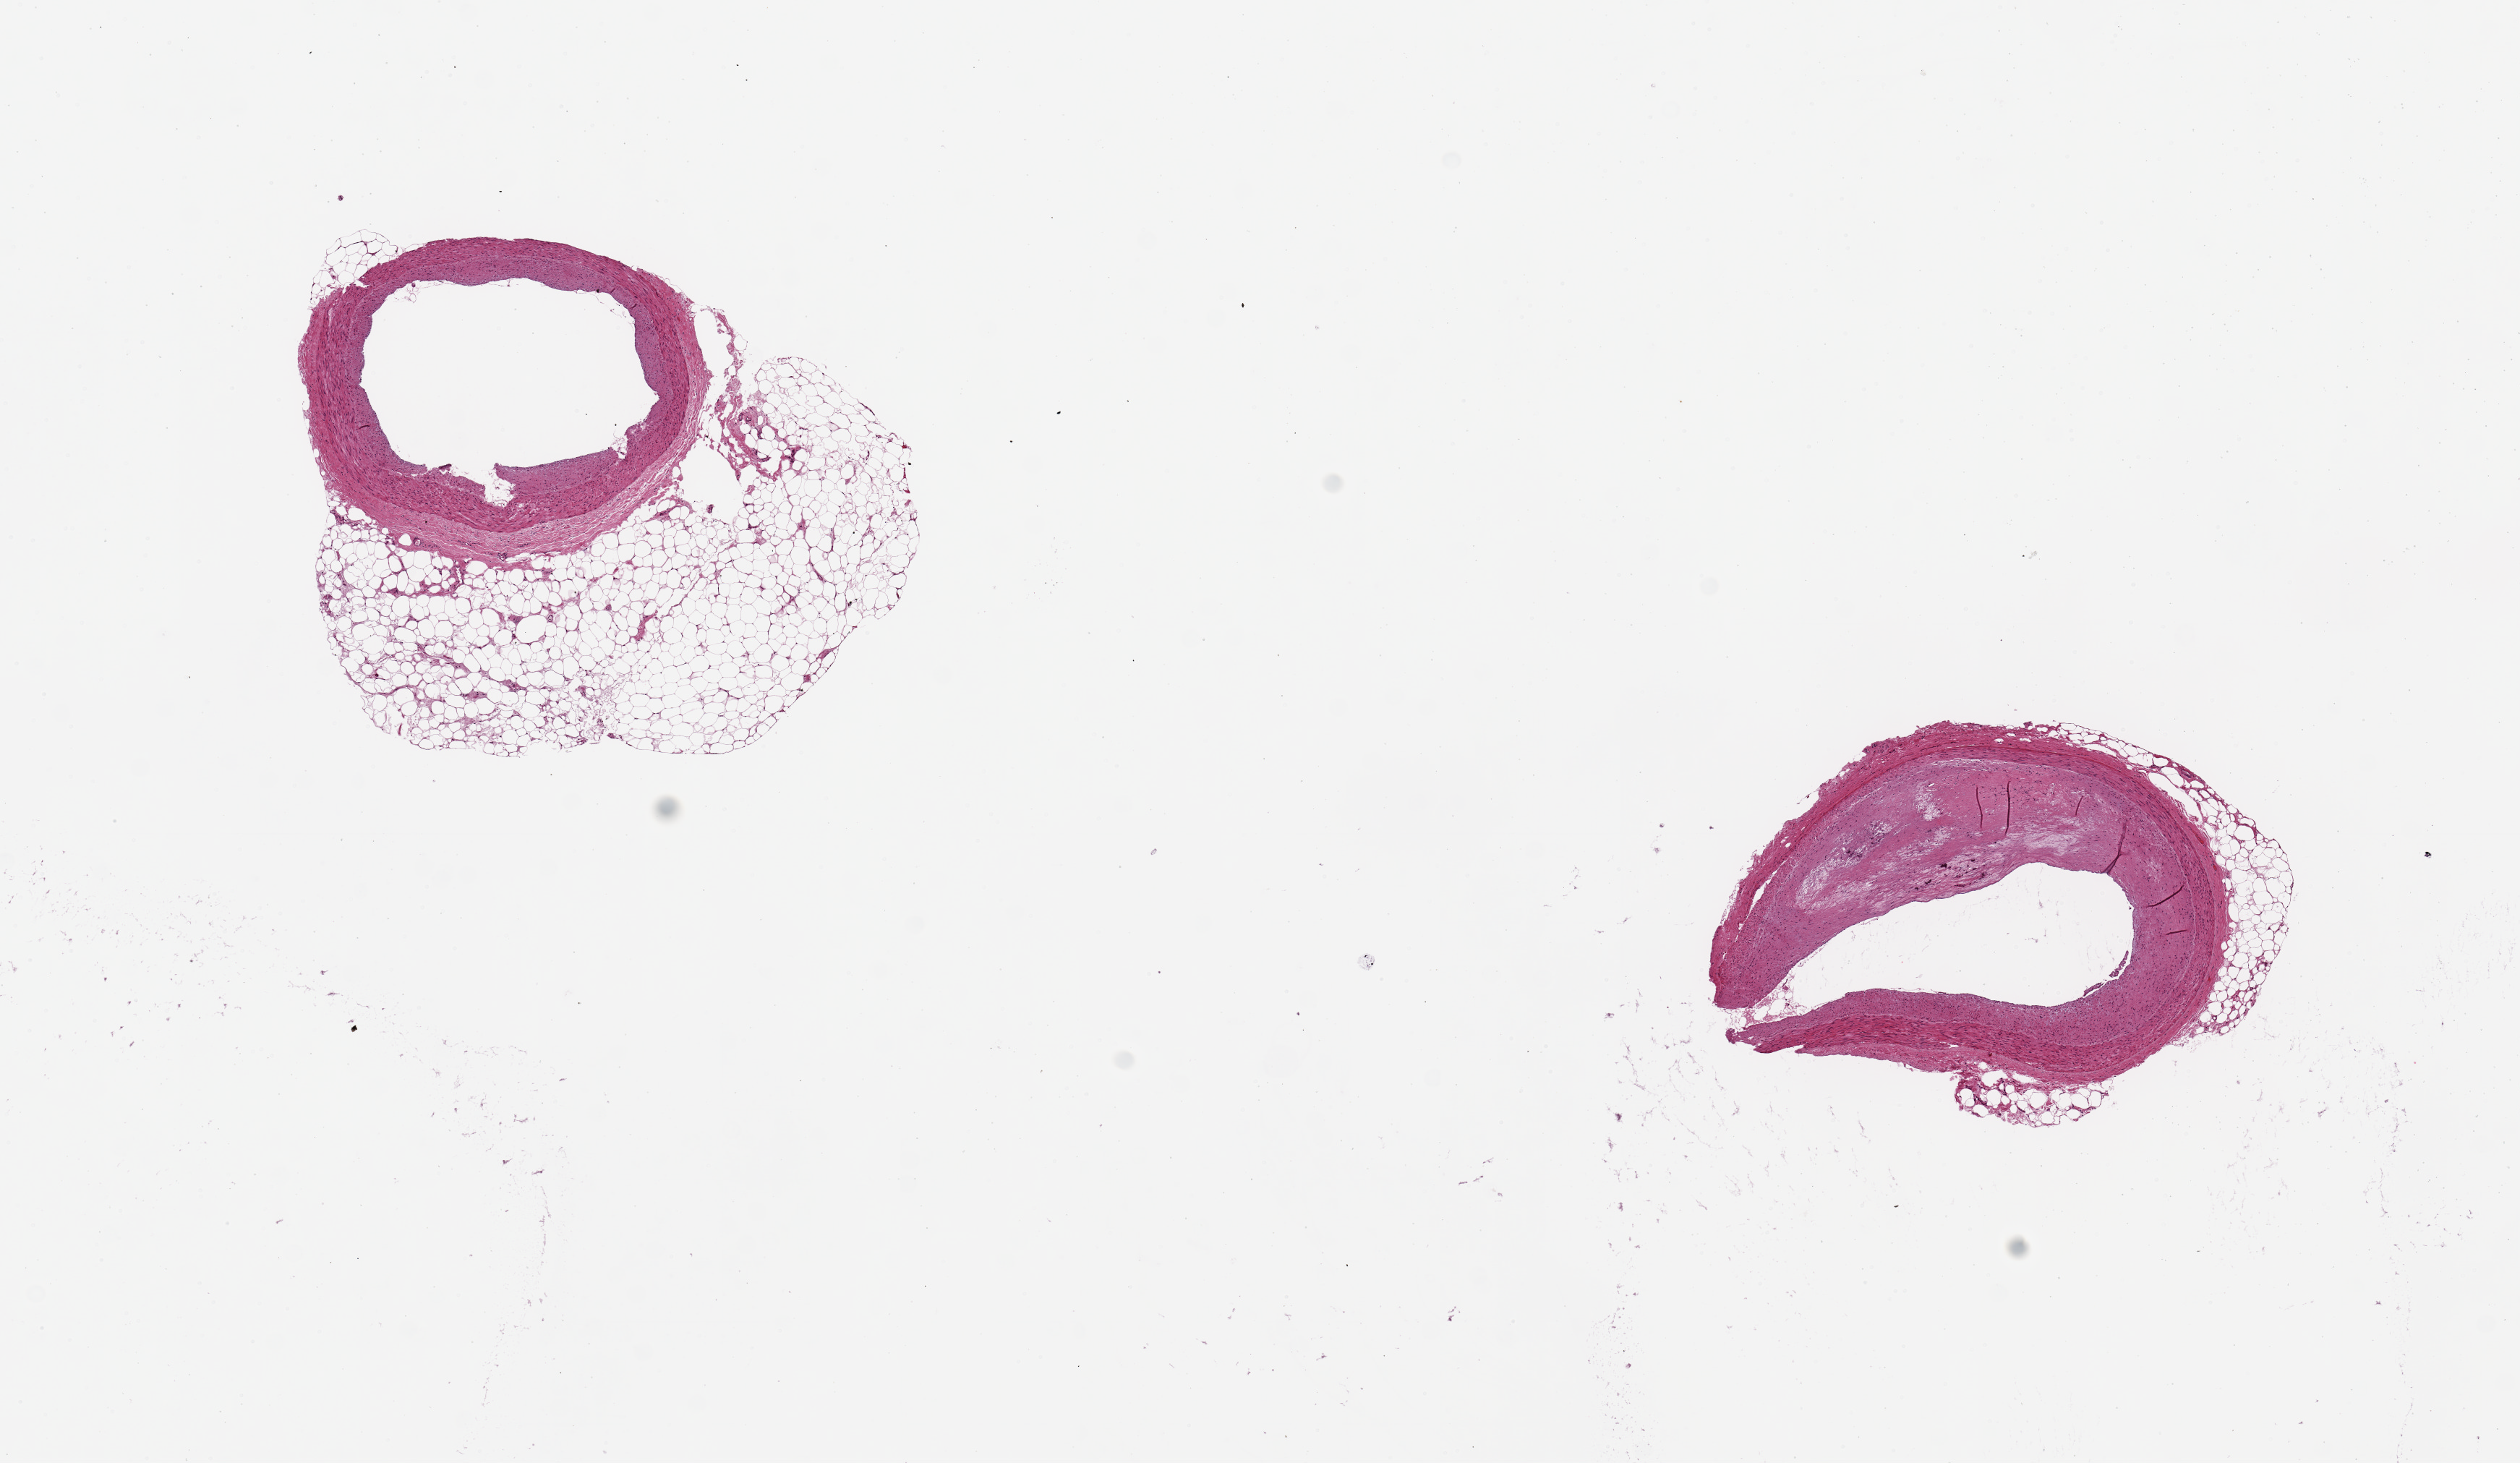
Digitized haematoxylin and eosin-stained section, a low-resolution overview of the entire scanned area, about 13.8 x 8.0 mm (from a 20x scan), PAXgene-fixed paraffin-embedded (PFPE) section, target tissue: coronary artery, tissue donor sample.
• reviewer comment on this tissue sample: 2 pieces, 4x3 & 3x2mm; up to 7mm layer atherosis, focally calcified